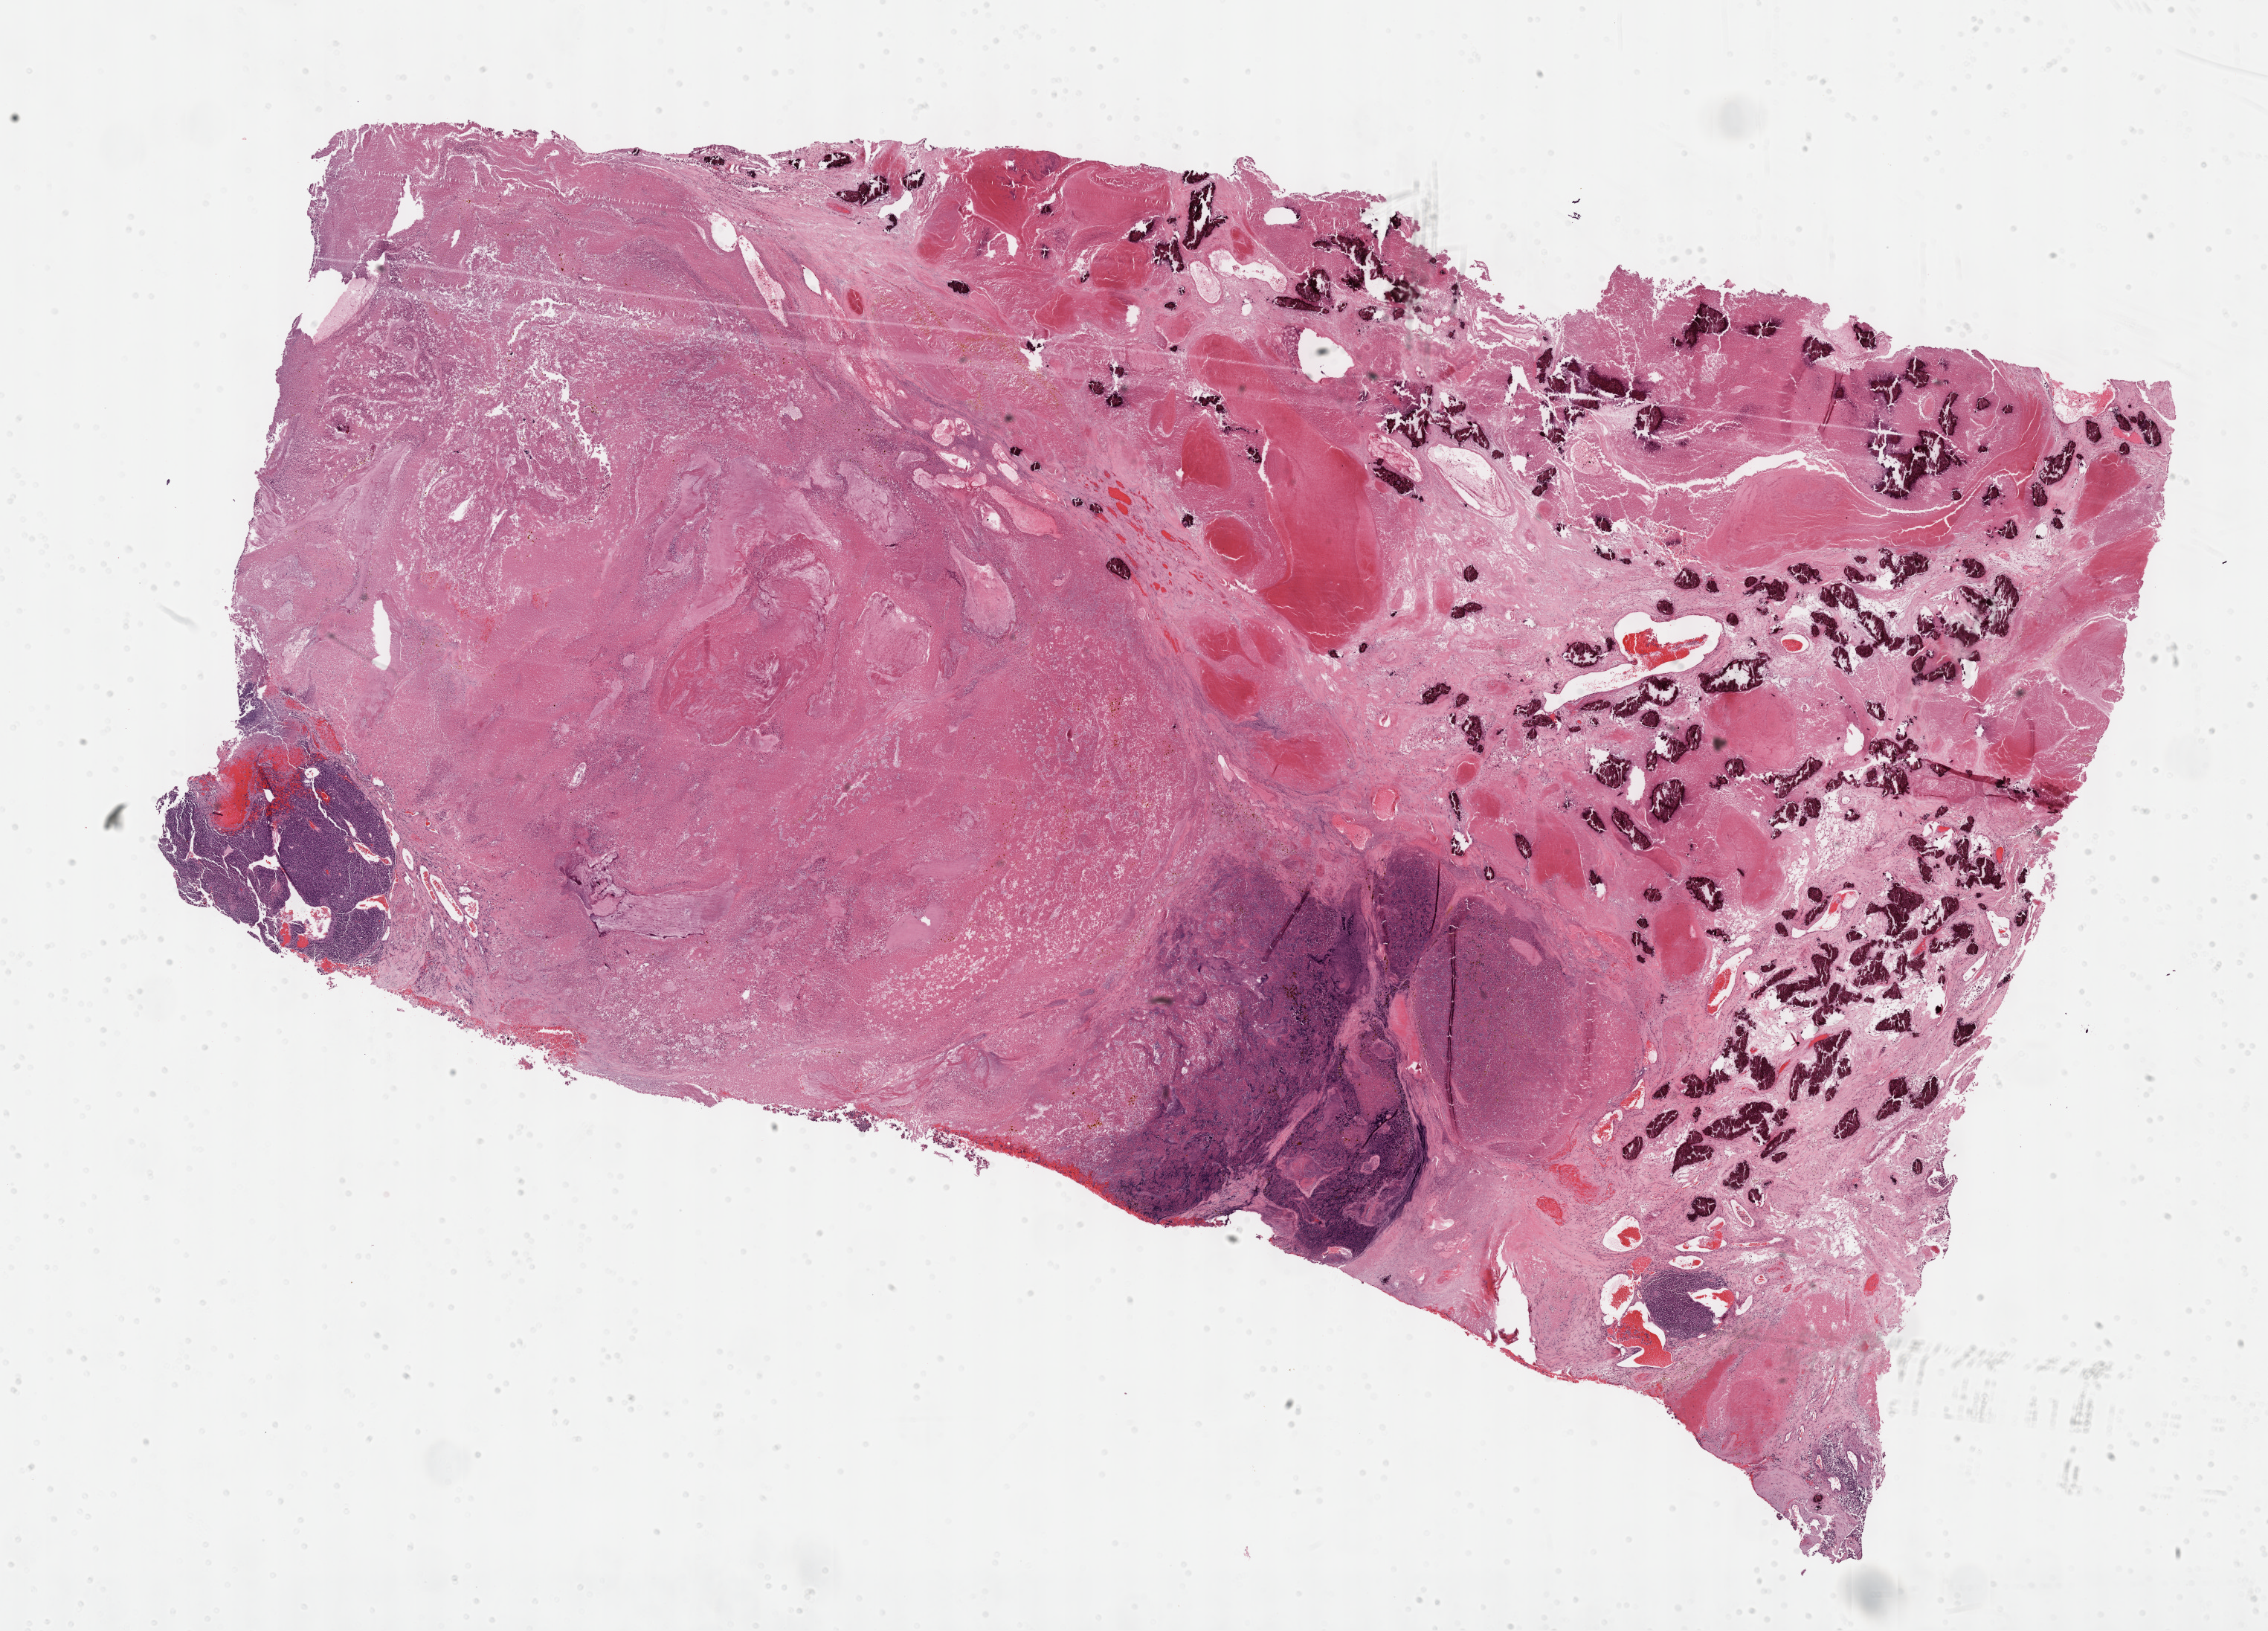
H&E-stained whole-slide image — a low-resolution overview of the entire scanned area, about 24.7 x 17.7 mm. Formalin-fixed paraffin-embedded (FFPE) diagnostic section. Sample: primary tumour, adrenal cortex. Female, age 32 years at initial diagnosis.
- lymph nodes positive (case pathology): 0 of 1 examined
- laterality: right
- pathologic diagnosis: Adrenal cortical carcinoma